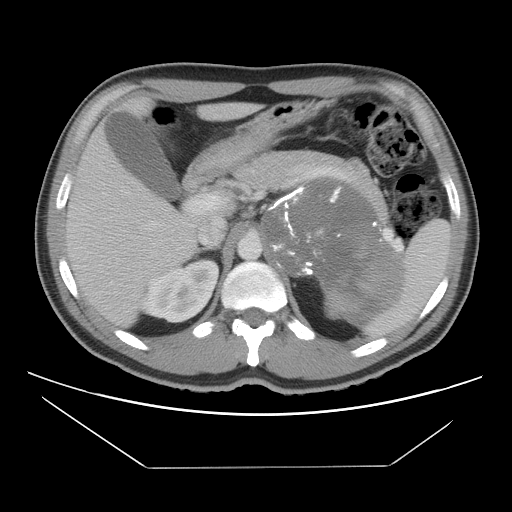
Contrast-enhanced abdominal CT, one axial slice. Slice 72 of 131 in the series (ordered by position). Reconstruction kernel STANDARD. 120 kVp. Intravenous contrast given. Soft-tissue window (W 400 / L 40 HU). 5 mm slice thickness. 512 × 512 image matrix. Male patient, age 44 years. From the clinical record (not read from this slice): diagnosis: adrenocortical carcinoma; tumour side: left adrenal; tumour size at pathology: 15.5 cm.
Annotated regions visible in this slice (semi-automatic segmentation, software-assisted and operator-edited):
- mass: box from (x=263, y=177) to (x=401, y=326) px